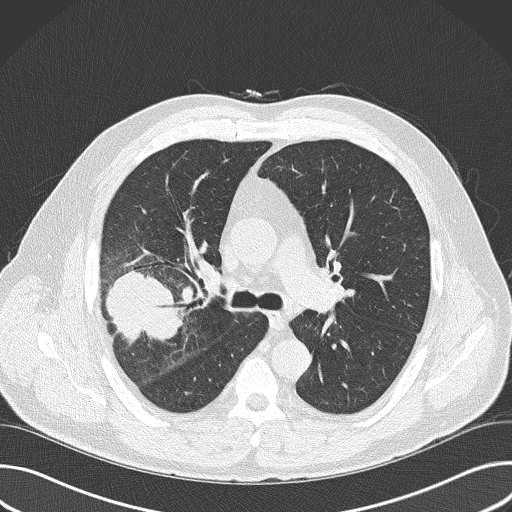
Chest CT (low-dose screening protocol), one axial image; first (baseline) screen; lung window (W 1500 / L -600 HU); slice 103 of 157 in the series. Male participant, aged 56 years at enrolment. Current smoker at enrolment.
- Expert reader's lesion annotation, bounding box (x1, y1, x2, y2) in pixels: (81, 262, 185, 369).
- Reader record for this screening exam (exam-level; its link to the box is not recorded): non-calcified nodule or mass ≥4 mm, right upper lobe, 6 × 5 mm, spiculated (stellate) margins, soft tissue attenuation.
- Lung cancer was diagnosed 16 days after this screen: adenocarcinoma, NOS, right upper lobe, poorly differentiated (G3), stage IIB (AJCC 6th edition), 60 mm at pathology.